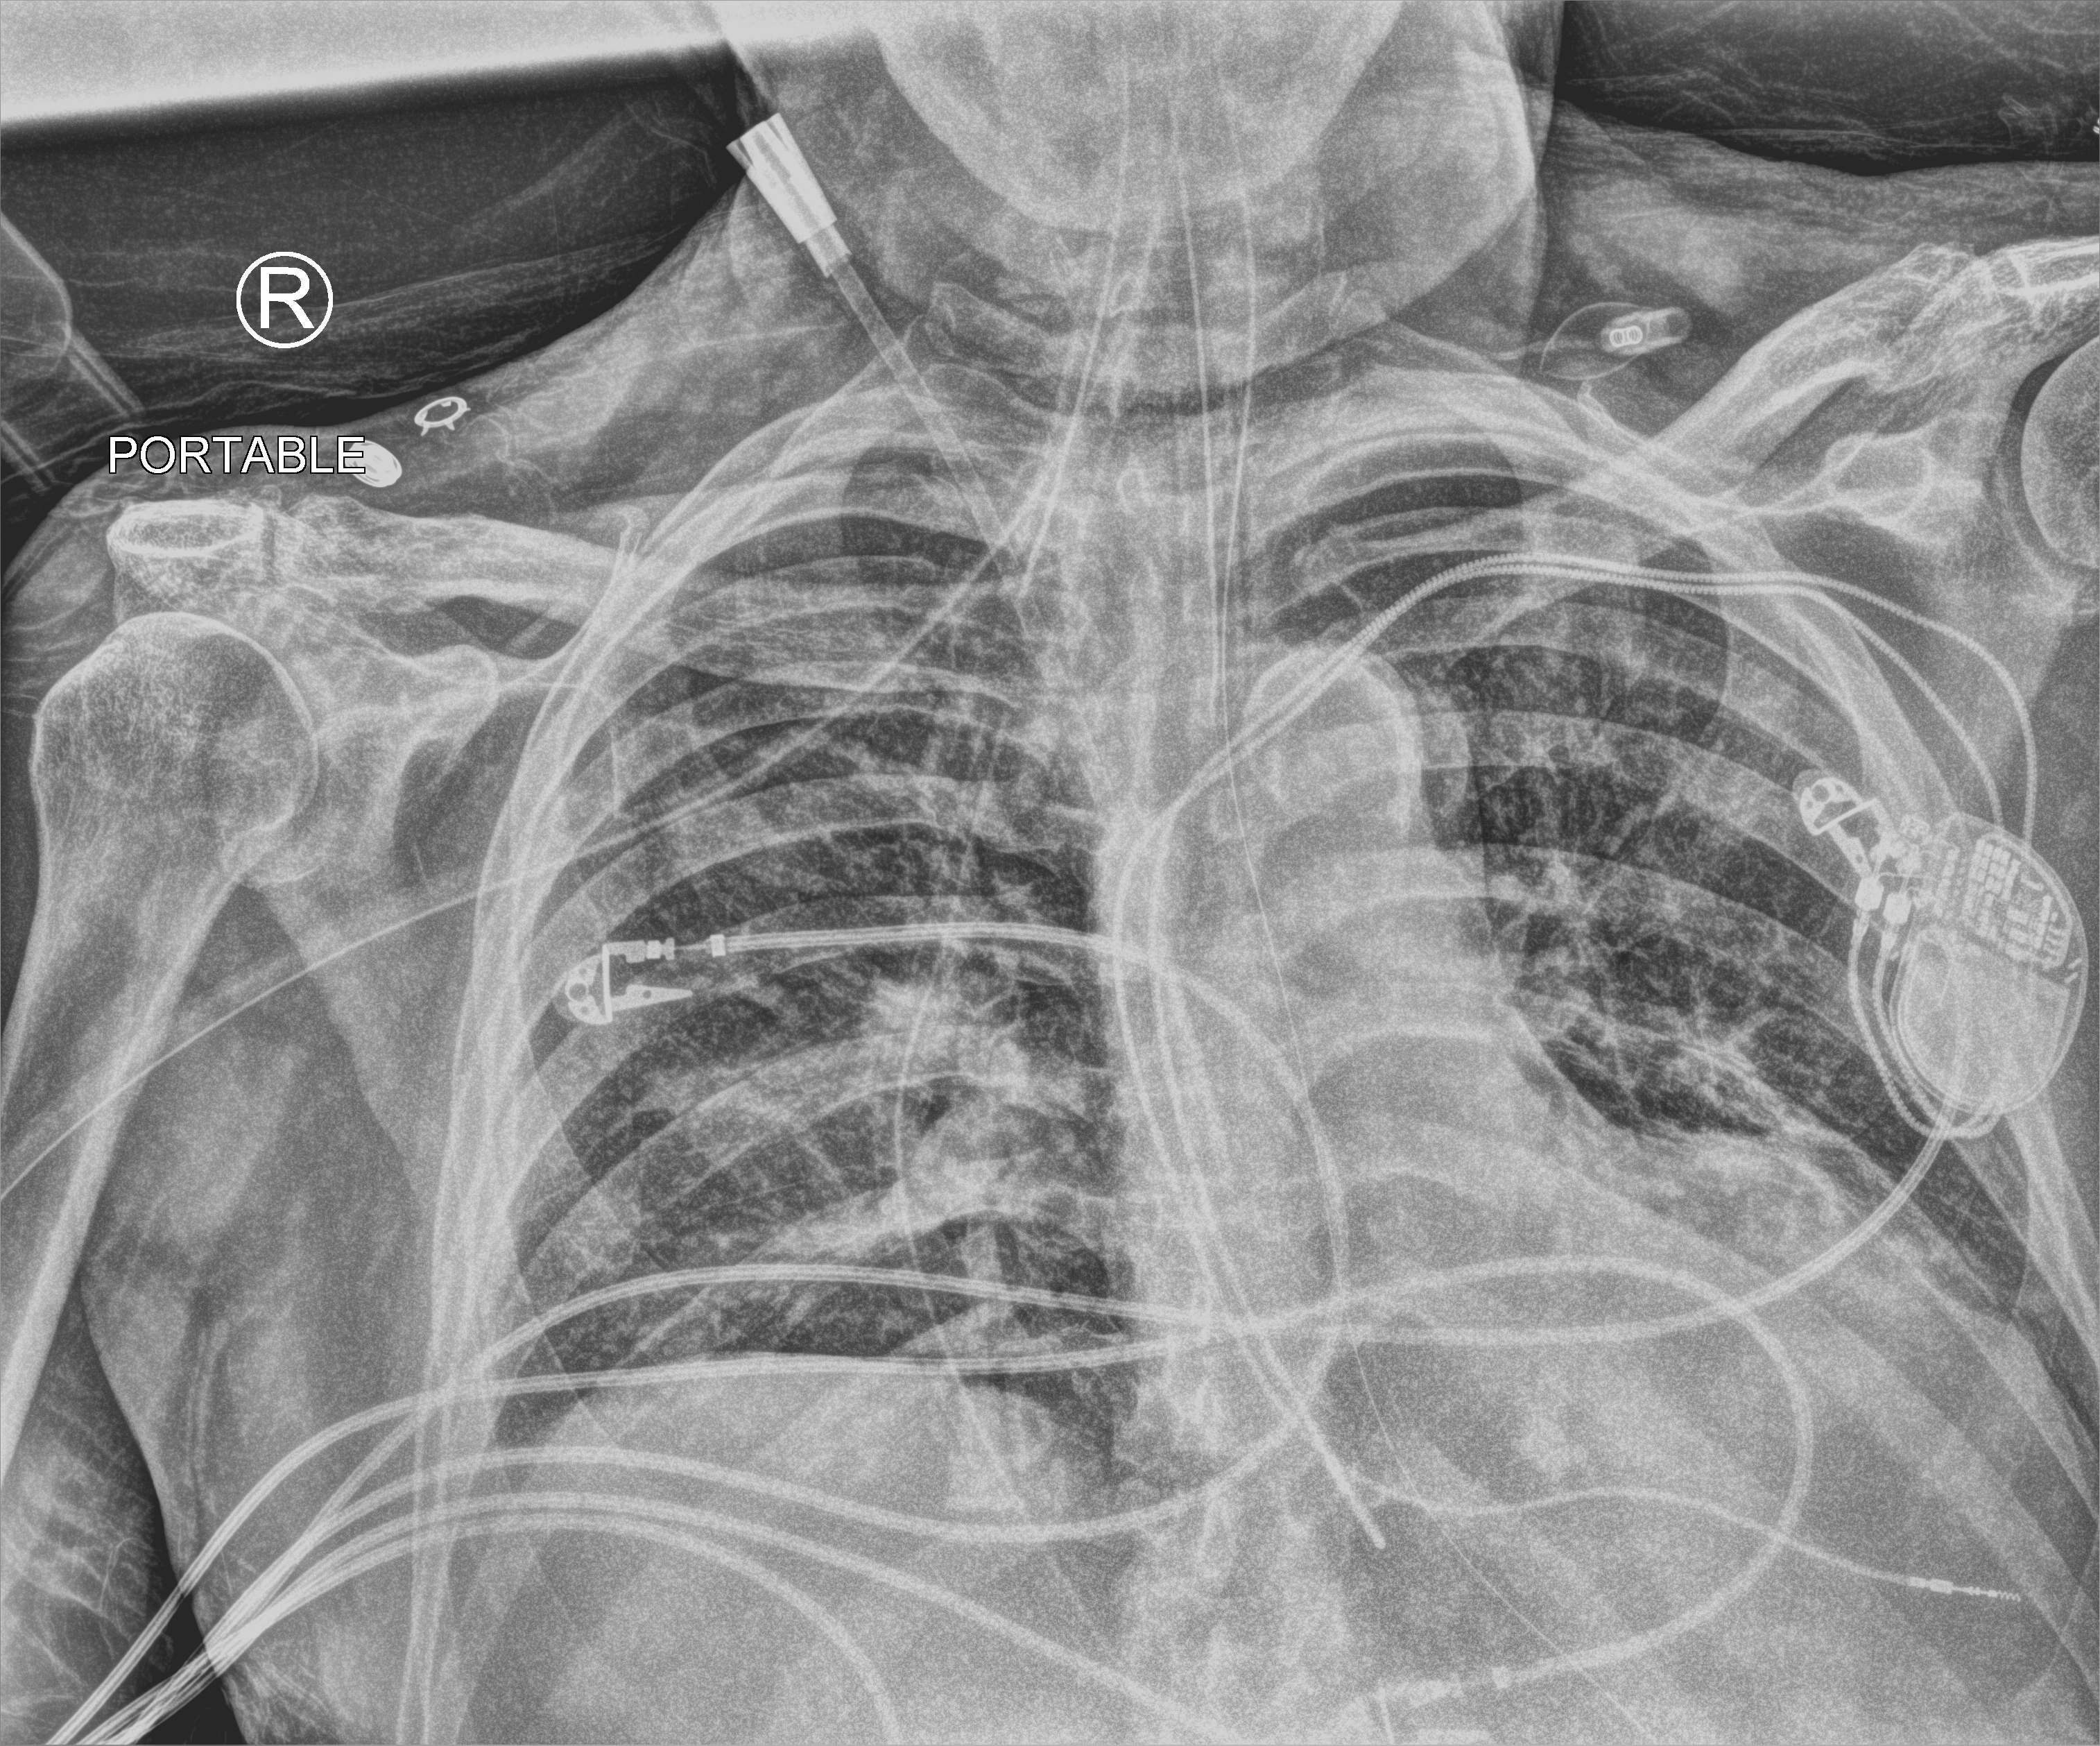
Portable chest radiograph, anteroposterior (AP) projection. Patient hospitalised with COVID-19; male, aged 60–74 years.
Hospital-stay facts (about this admission, not read from this image; timing relative to this image not recorded):
- mechanically ventilated during this hospital stay: yes
- admitted to intensive care during this hospital stay: yes